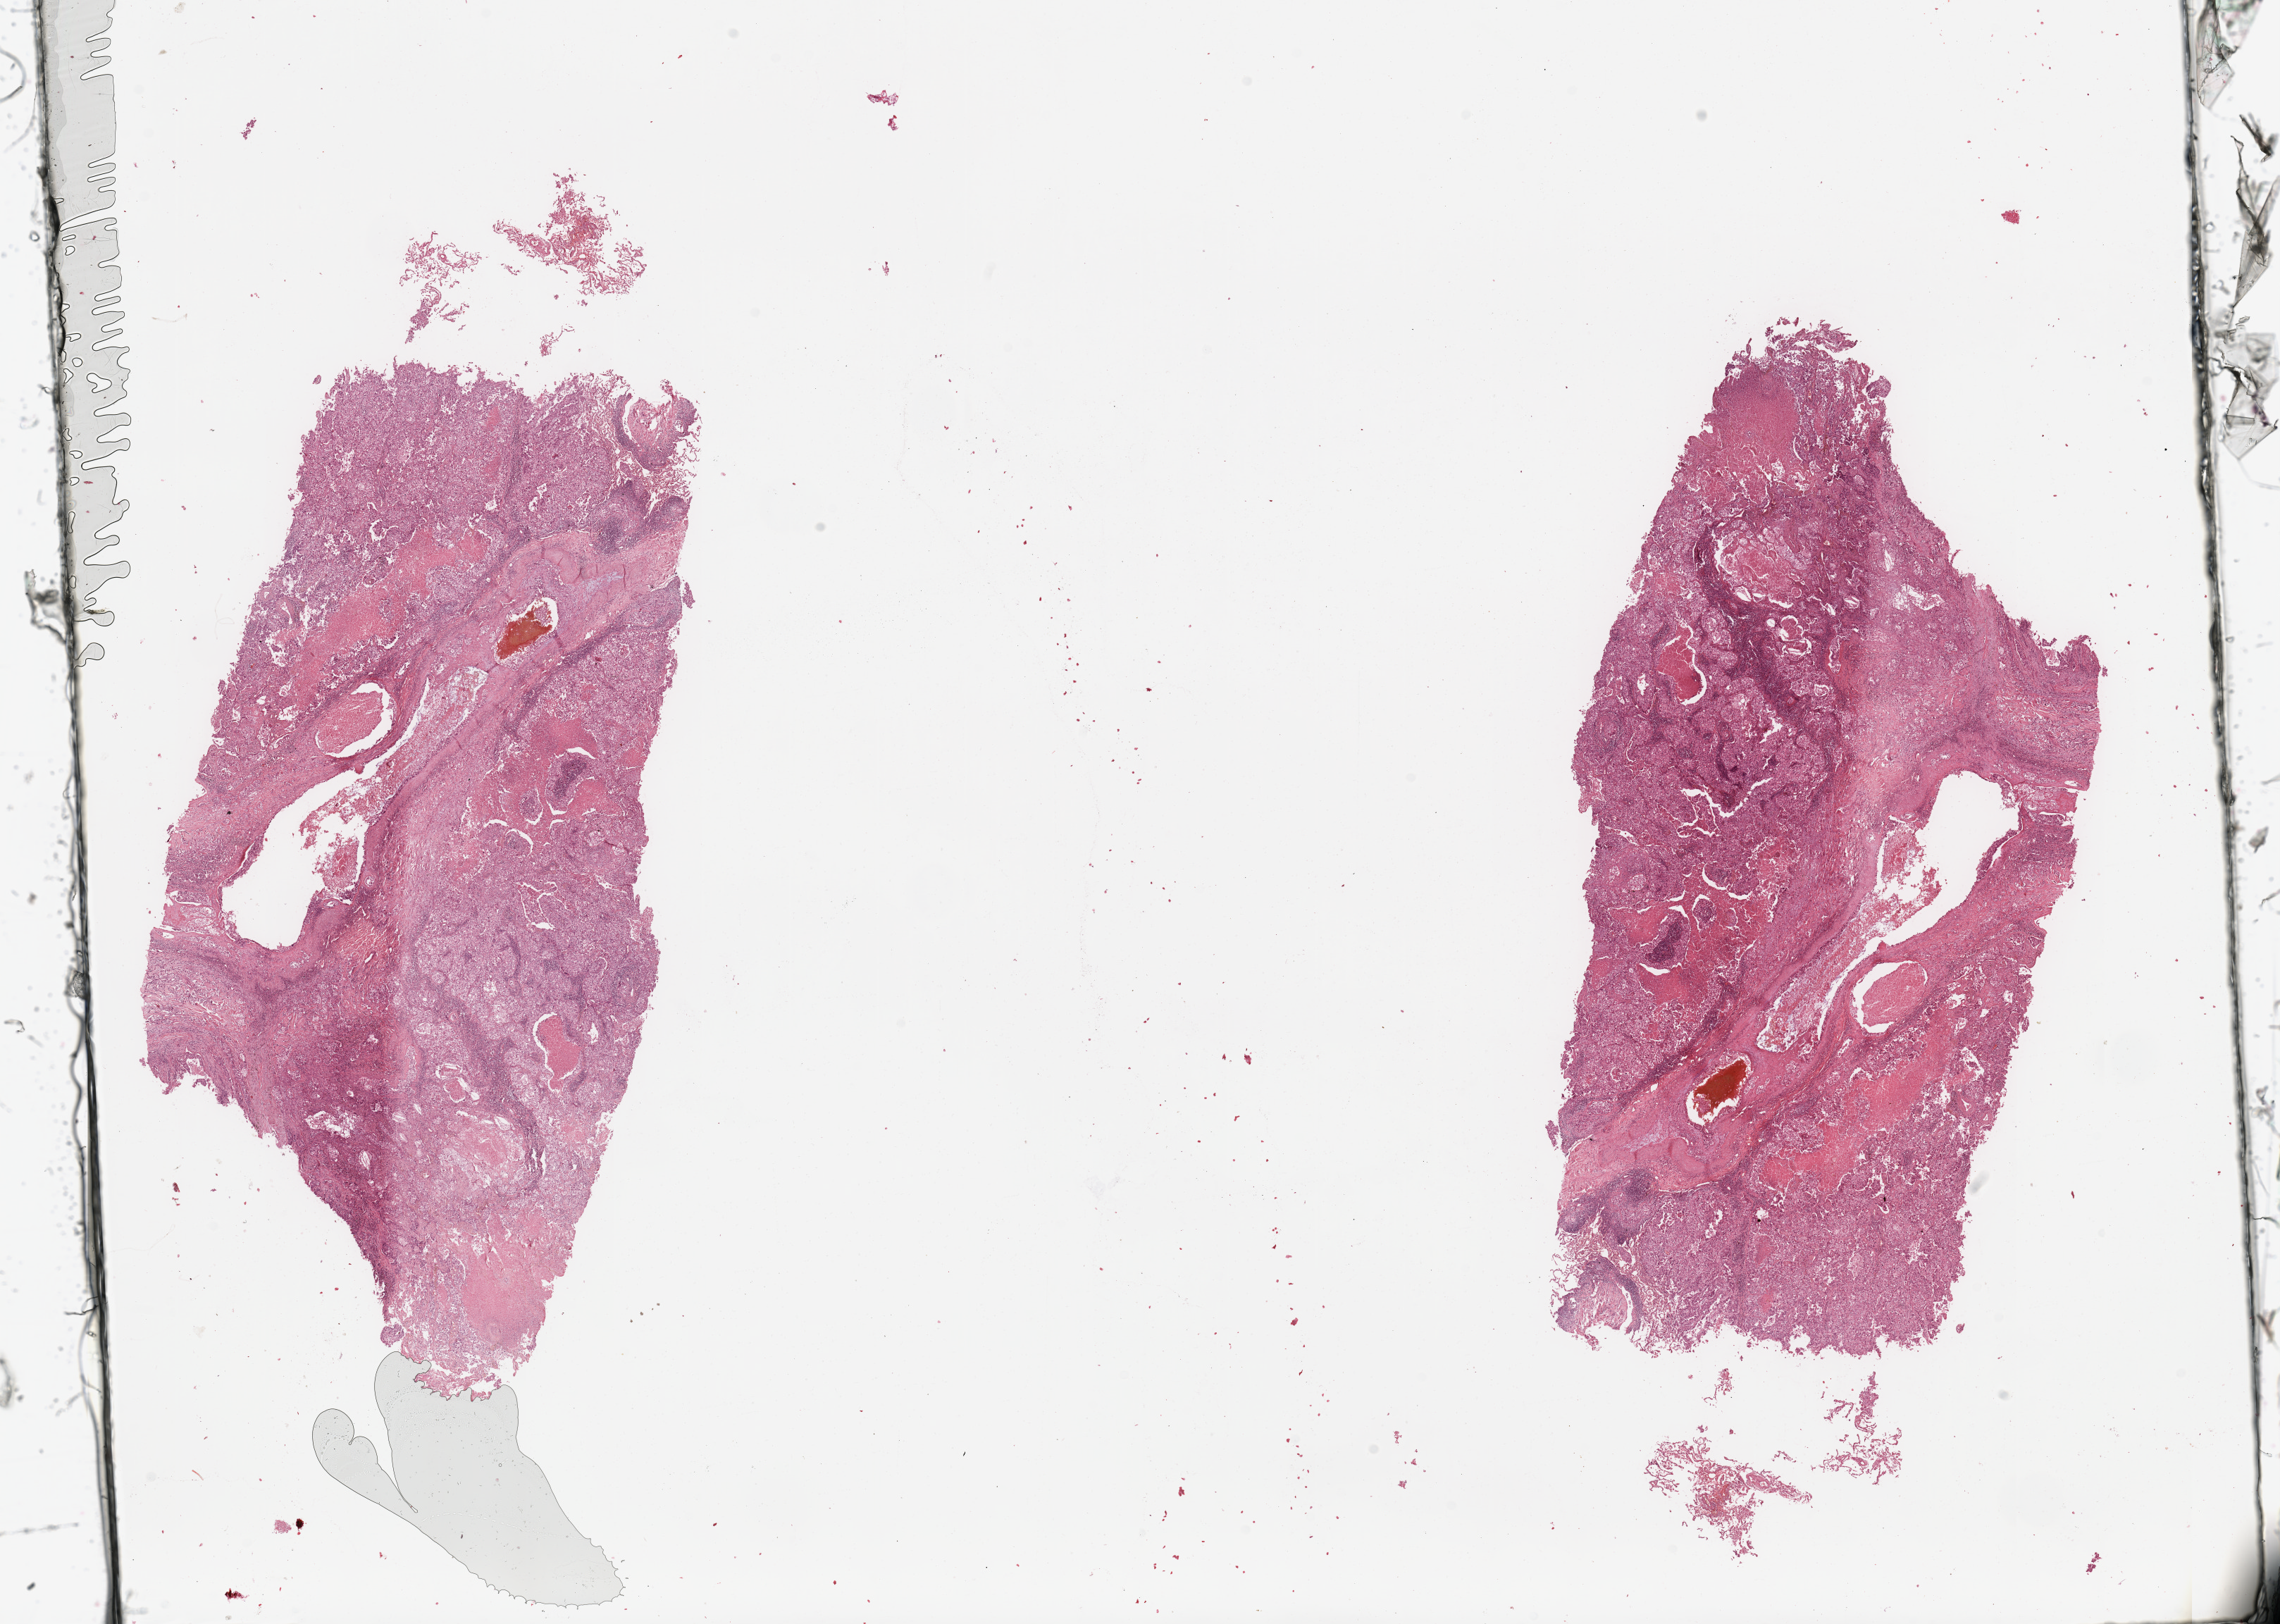
H&E whole-slide image, shown as a low-resolution overview of the whole scanned area (about 25.6 x 18.2 mm, slide scanned at 20x), tumour tissue sample, lung. Patient: male, age 72 years. Histologic grade: G2 (moderately differentiated).
• diagnosis: Adenocarcinoma, NOS
• AJCC pathologic stage: IB
• primary tumour site (as recorded): left lower lobe